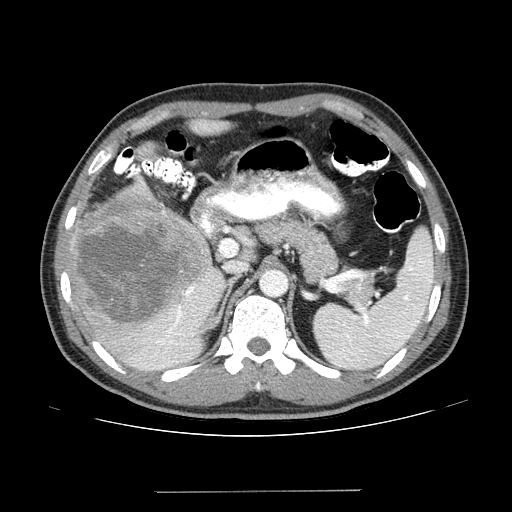
Contrast-enhanced abdominal CT (liver protocol), one axial slice; slice 85 of 131 in the series (ordered by position); one of 2 acquisitions stored at this slice position; soft-tissue window (W 400 / L 40 HU); 512 × 512 image matrix, field of view 380 × 380 mm. Case-level facts recorded for this patient, not image findings: diagnosis: hepatocellular carcinoma (patient treated with transarterial chemoembolisation; whether this scan precedes or follows treatment is not stated here); TNM stage (as recorded): Stage-I; Child-Pugh class: A.
Outlined on this slice (semi-automatic segmentation, software-assisted and operator-edited):
- liver parenchyma outside the tumour (the mass and vessels are separate outlines, so this box may not span the whole liver): box from (x=68, y=180) to (x=224, y=370) px
- mass: (x=68, y=187)–(x=211, y=327)
- liver vessels: (x=150, y=291)–(x=192, y=367)